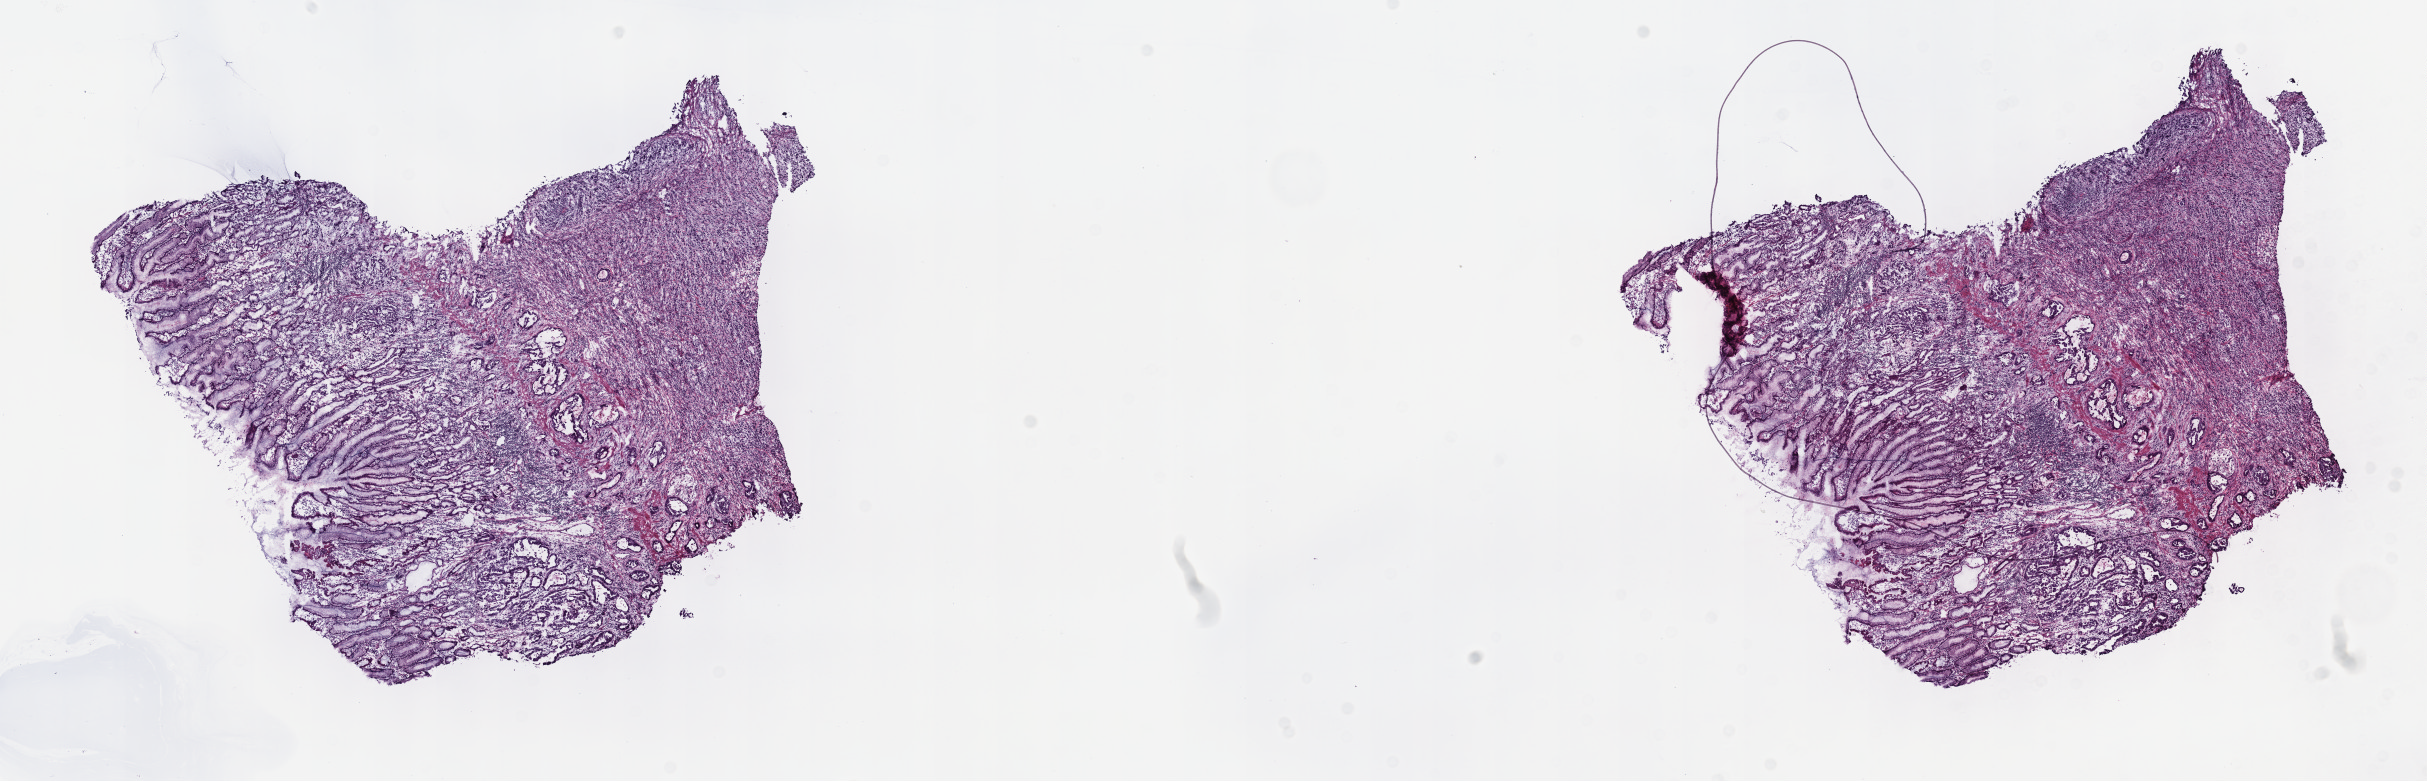
Digitized H&E-stained tissue section (whole slide), low-resolution overview of the scanned area, about 19.6 x 6.3 mm (from a 40x scan). Frozen section from the top of the tissue portion. Sample: primary tumour, stomach. Patient: male, age at initial diagnosis 70 years. Histologic grade: G3 (poorly differentiated). Composition of this section per pathologist review: tumour cells 40%, tumour nuclei 60%, normal cells 60%, stromal cells 0%, necrosis 0%. Infiltration values recorded for this section: lymphocyte infiltration 8%, monocyte infiltration 0%, neutrophil infiltration 0%.
• histologic diagnosis: Carcinoma, diffuse type (body of stomach)
• AJCC pathologic stage: IIIB (6th edition)